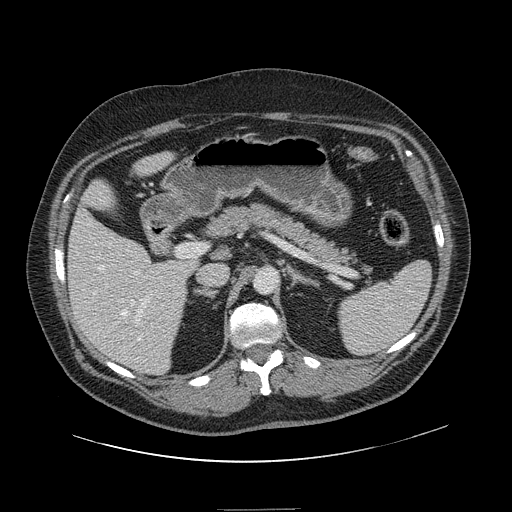
Contrast-enhanced abdominal CT, one axial slice; position 78 of 154 along the scan axis; intravenous contrast given; soft-tissue window (W 400 / L 40 HU); 2.5 mm slice thickness; 512 × 512 image matrix, field of view 451 × 451 mm. Male patient, age 61 years. Case-level facts recorded for this patient, not image findings: diagnosis: colorectal cancer liver metastases, imaged before liver resection; multiple liver metastases: yes; largest metastasis: 2.6 cm; disease in both lobes: yes.
Structures marked on this image (outlined manually by an expert reader):
- hepatic veins: bounding box (x1, y1, x2, y2) in pixels: (98, 265, 153, 341)
- liver: (68, 154, 197, 374)
- planned liver remnant (the part of the liver to remain after resection): (69, 154, 197, 365)
- portal vein (with intrahepatic branches): (93, 271, 150, 323)